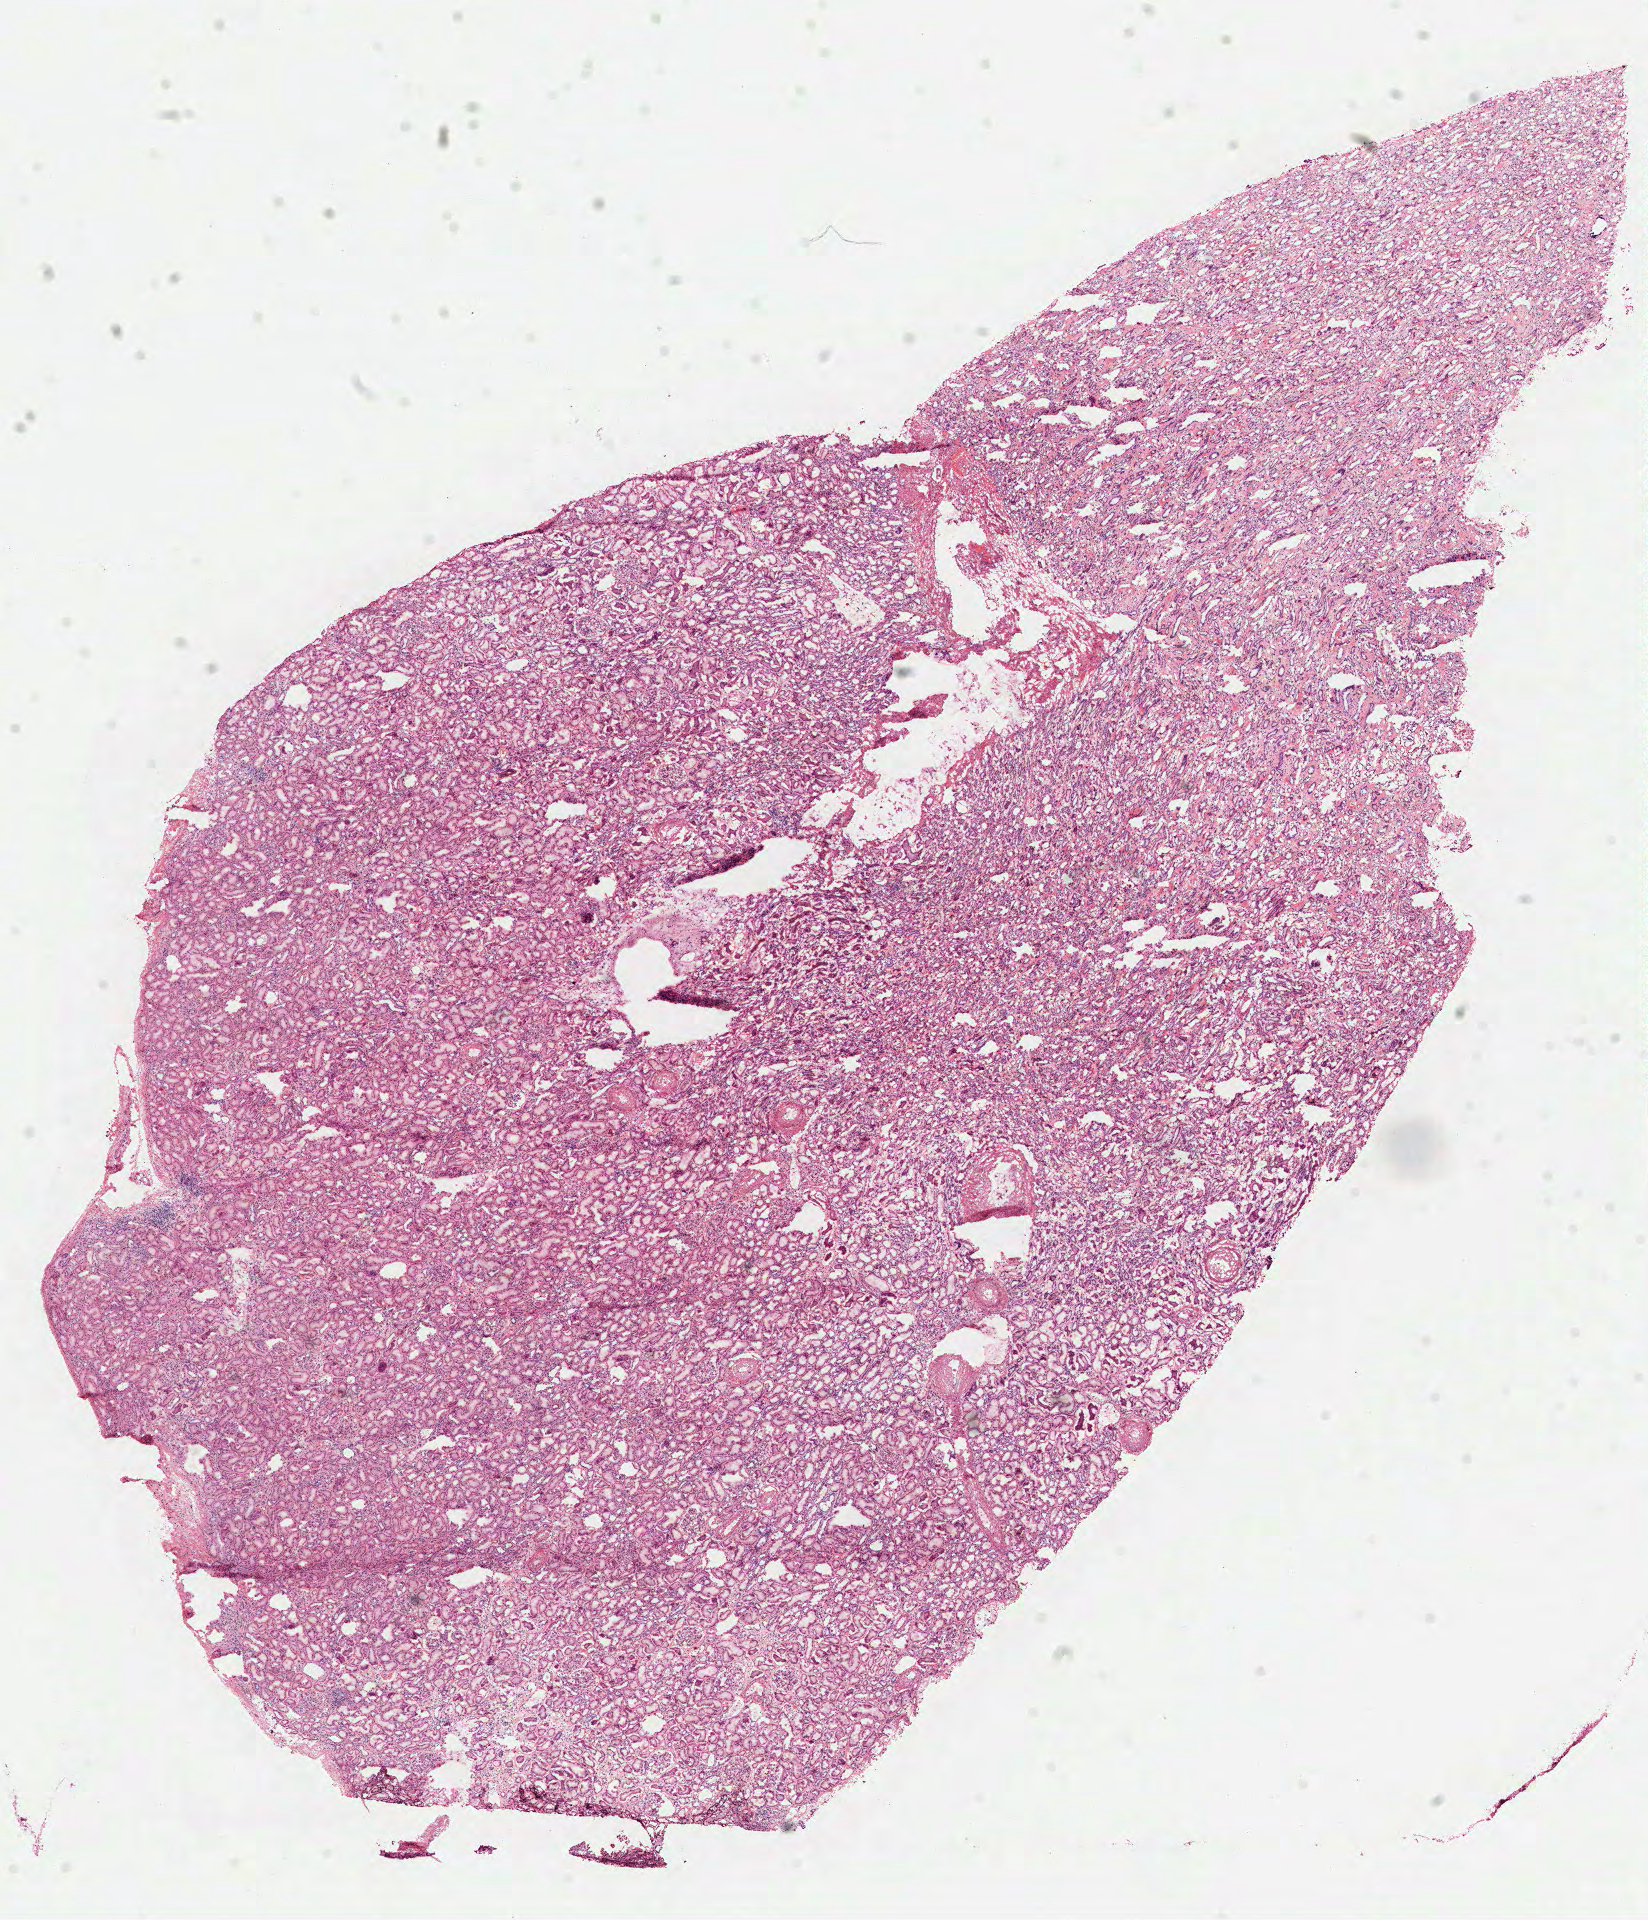
Whole-slide histology image, H&E-stained, low-resolution overview of the scanned area, about 13.3 x 15.5 mm; frozen section from the top of the tissue portion; sample: solid tissue normal (non-tumour tissue), kidney. Male, age 73 years at initial diagnosis.
This section: solid tissue normal (non-tumour) sample from the same patient. Patient diagnosis: Papillary adenocarcinoma, NOS.